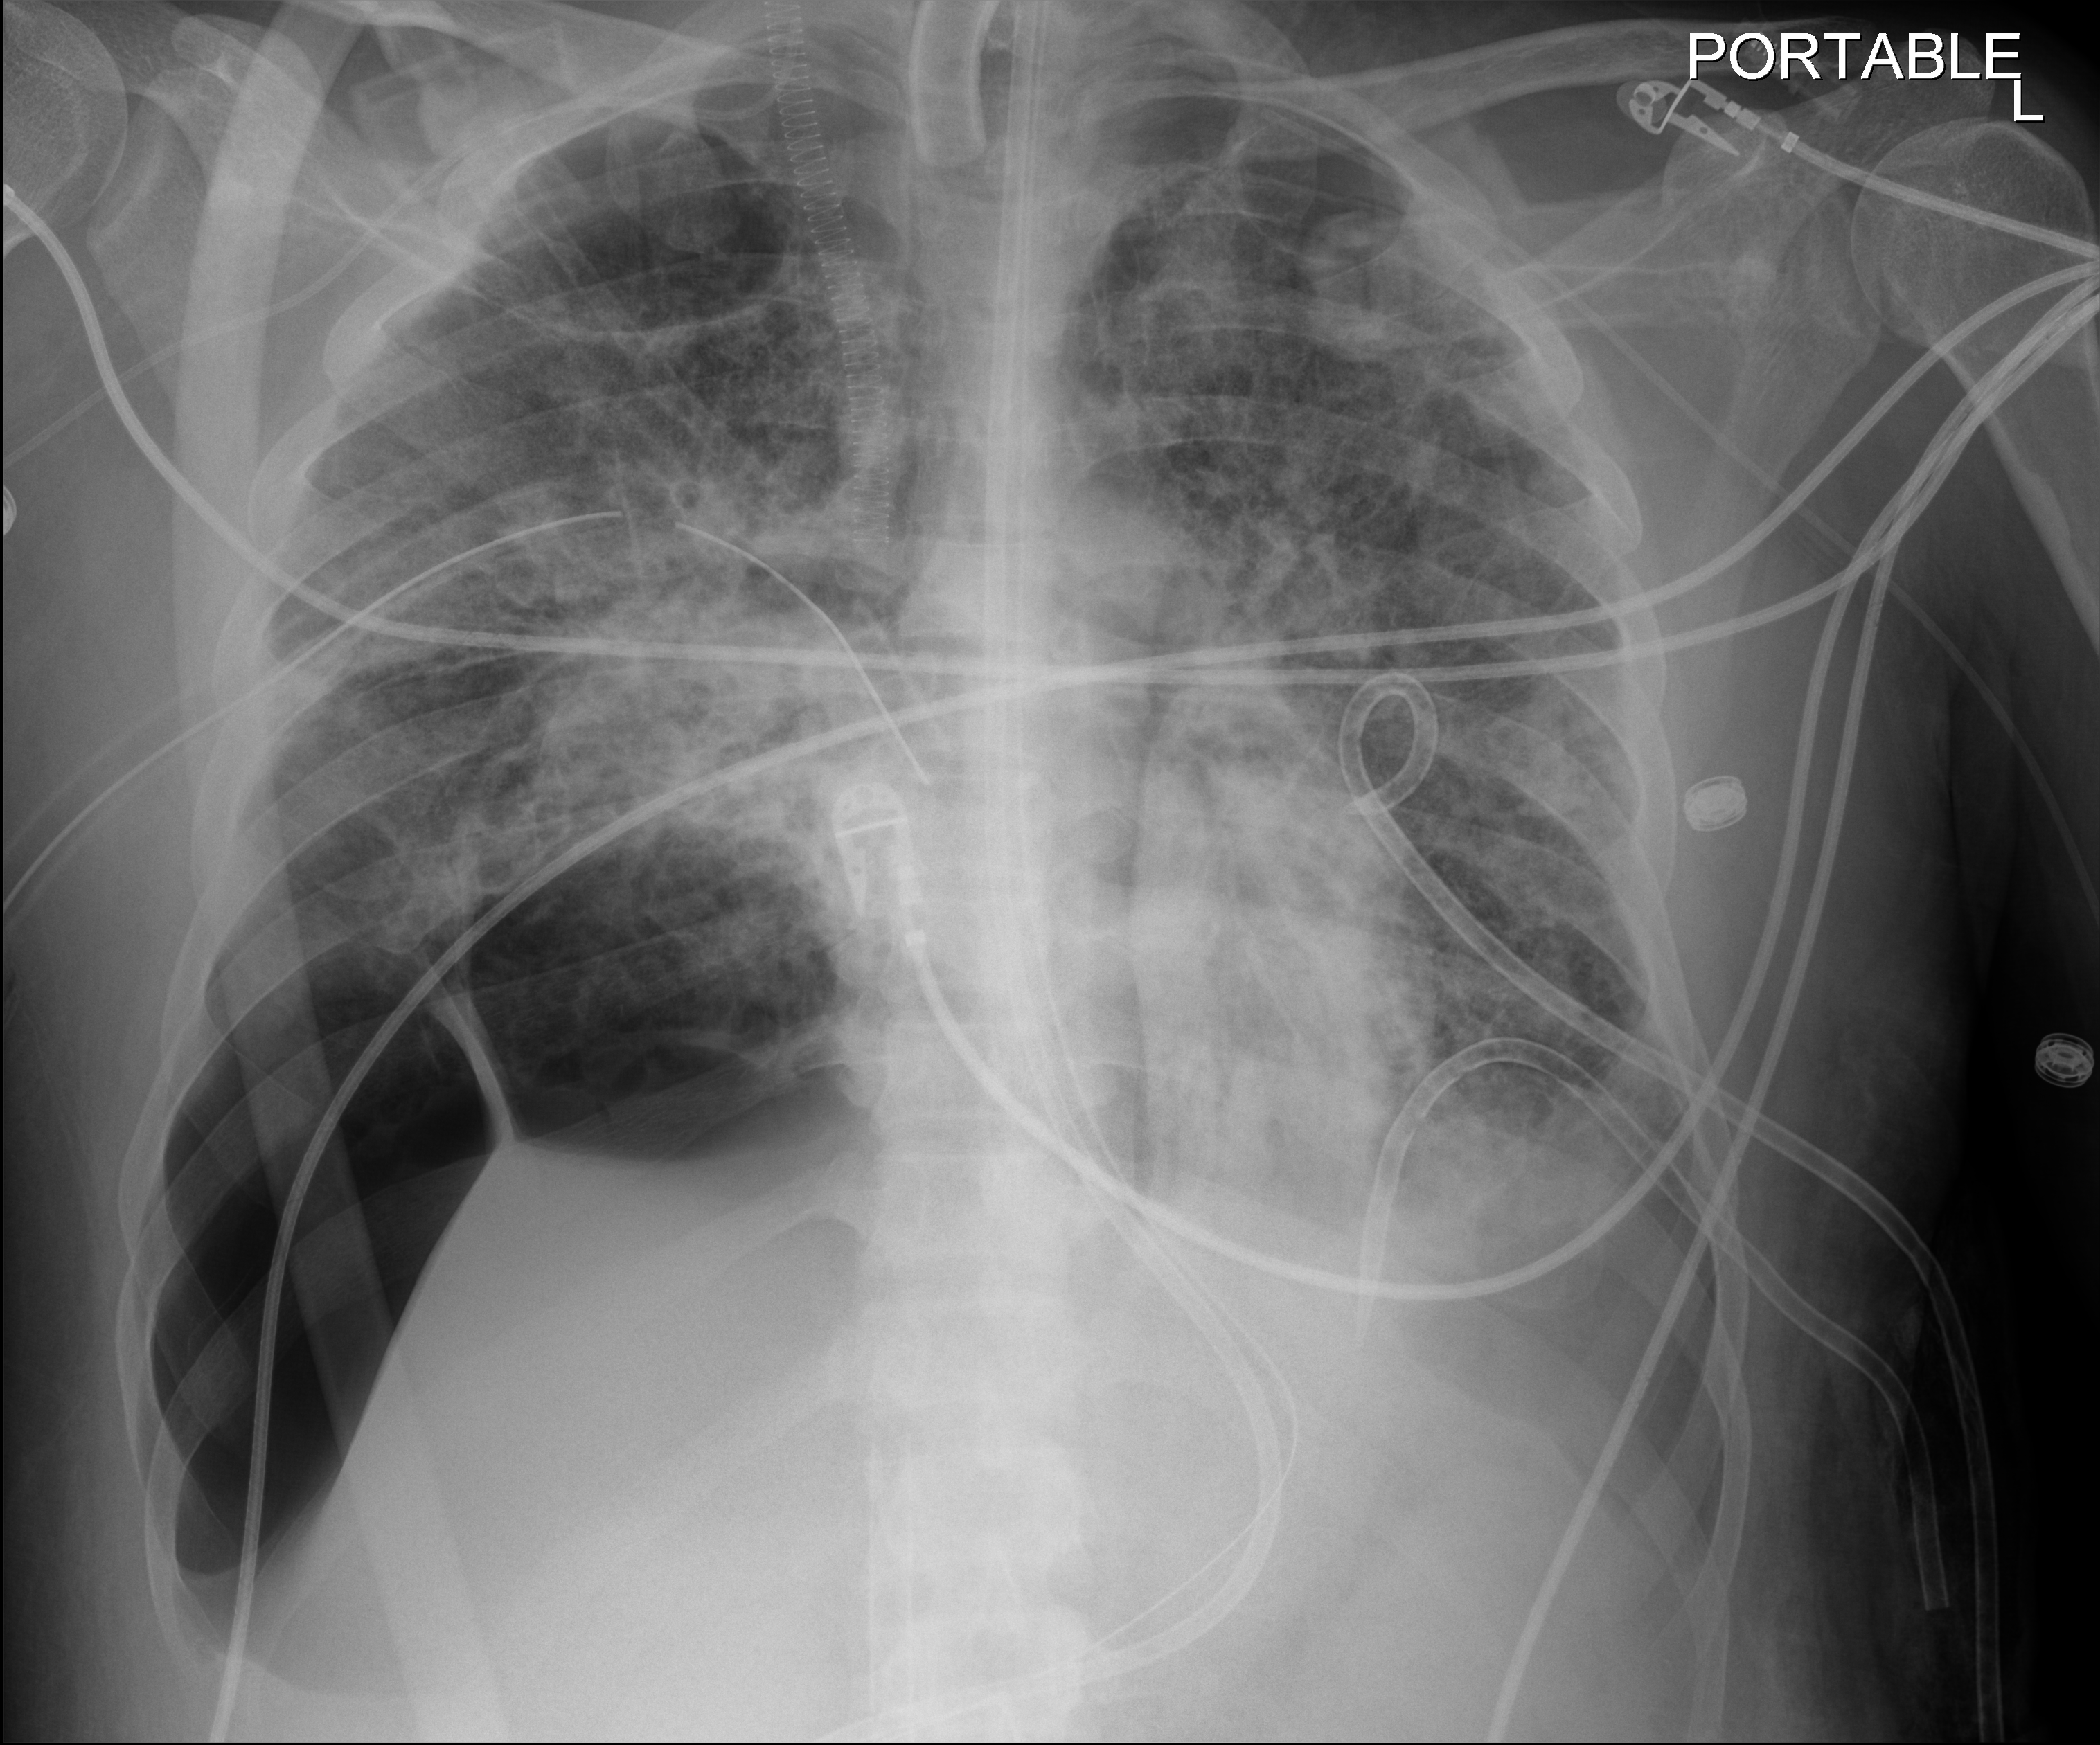
Bedside chest radiograph (digital radiography), anteroposterior (AP) projection. Adult patient hospitalised with COVID-19, age 18–59 years.
From the hospital-stay record, not from the radiograph (when in the stay this image was taken is not recorded):
- other chronic lung disease (admission record): no